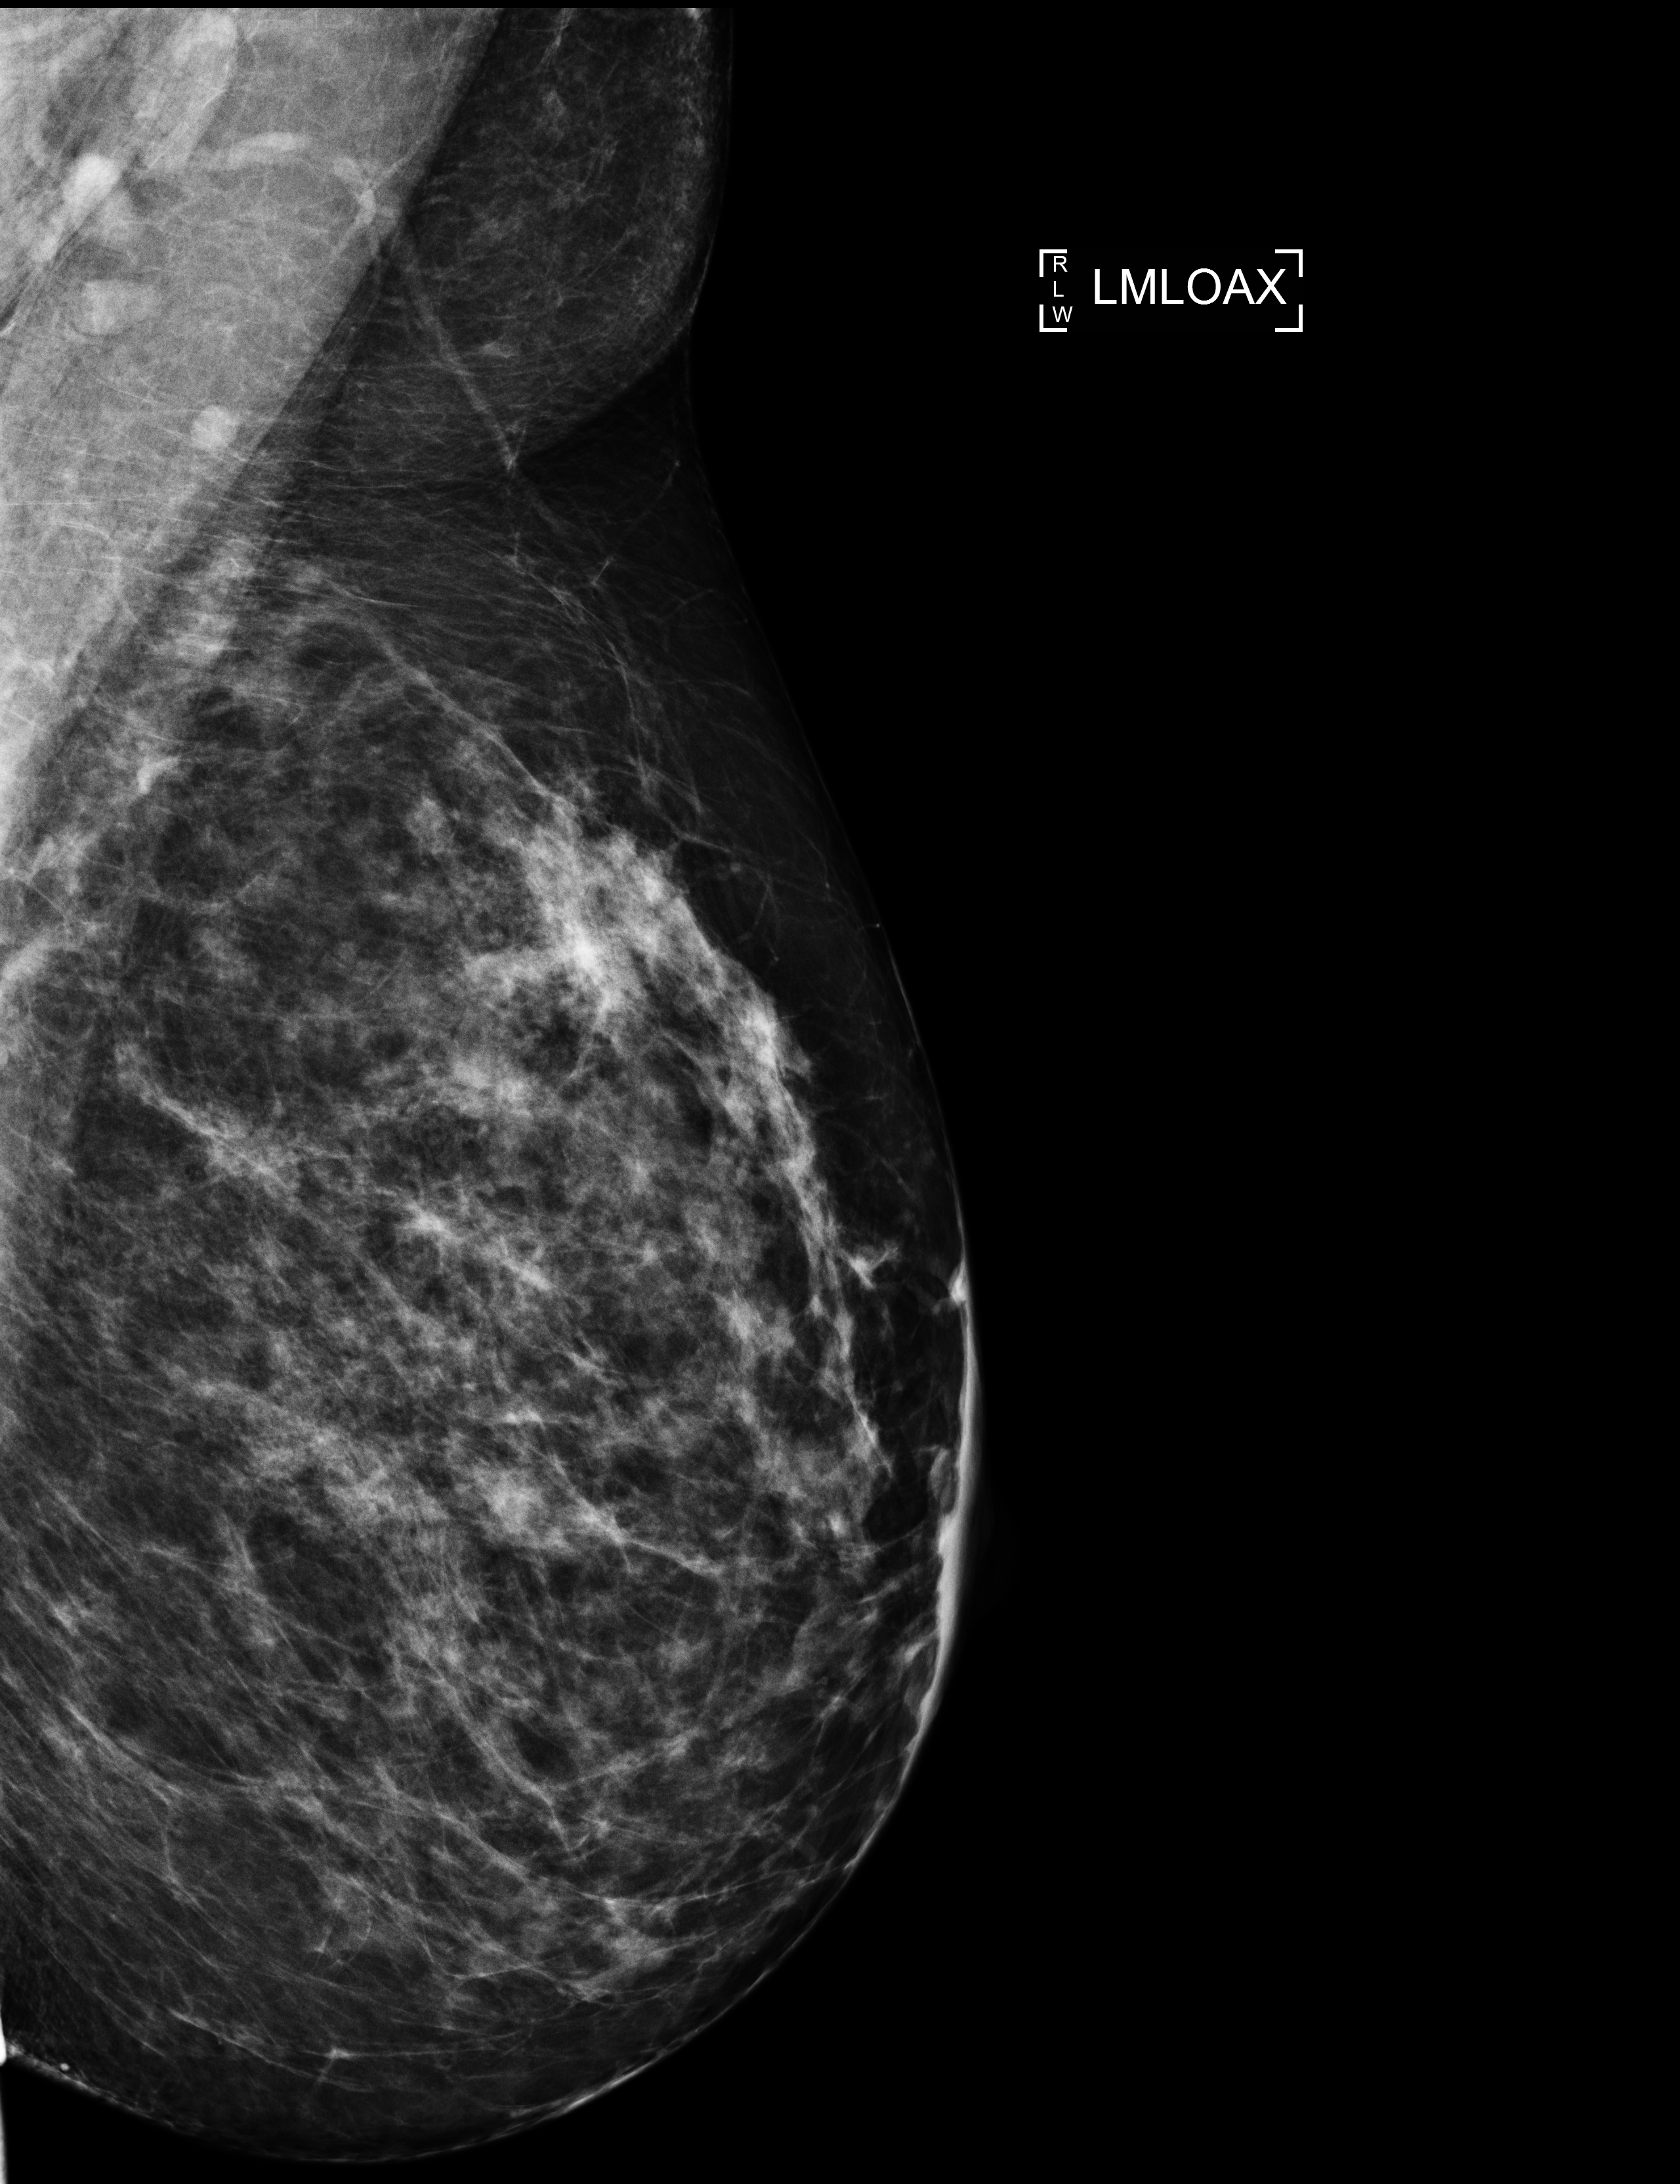
Digital mammogram (FFDM), left breast, medio-lateral oblique projection (axillary tissue), annual screening mammography examination. Female patient, age 48 years.
BI-RADS breast density category at the screening exam (both breasts, scale 1–4): 3. Final BI-RADS category for the screening round (tomosynthesis exam, both breasts): category 1. Recall: no recall after this screen.